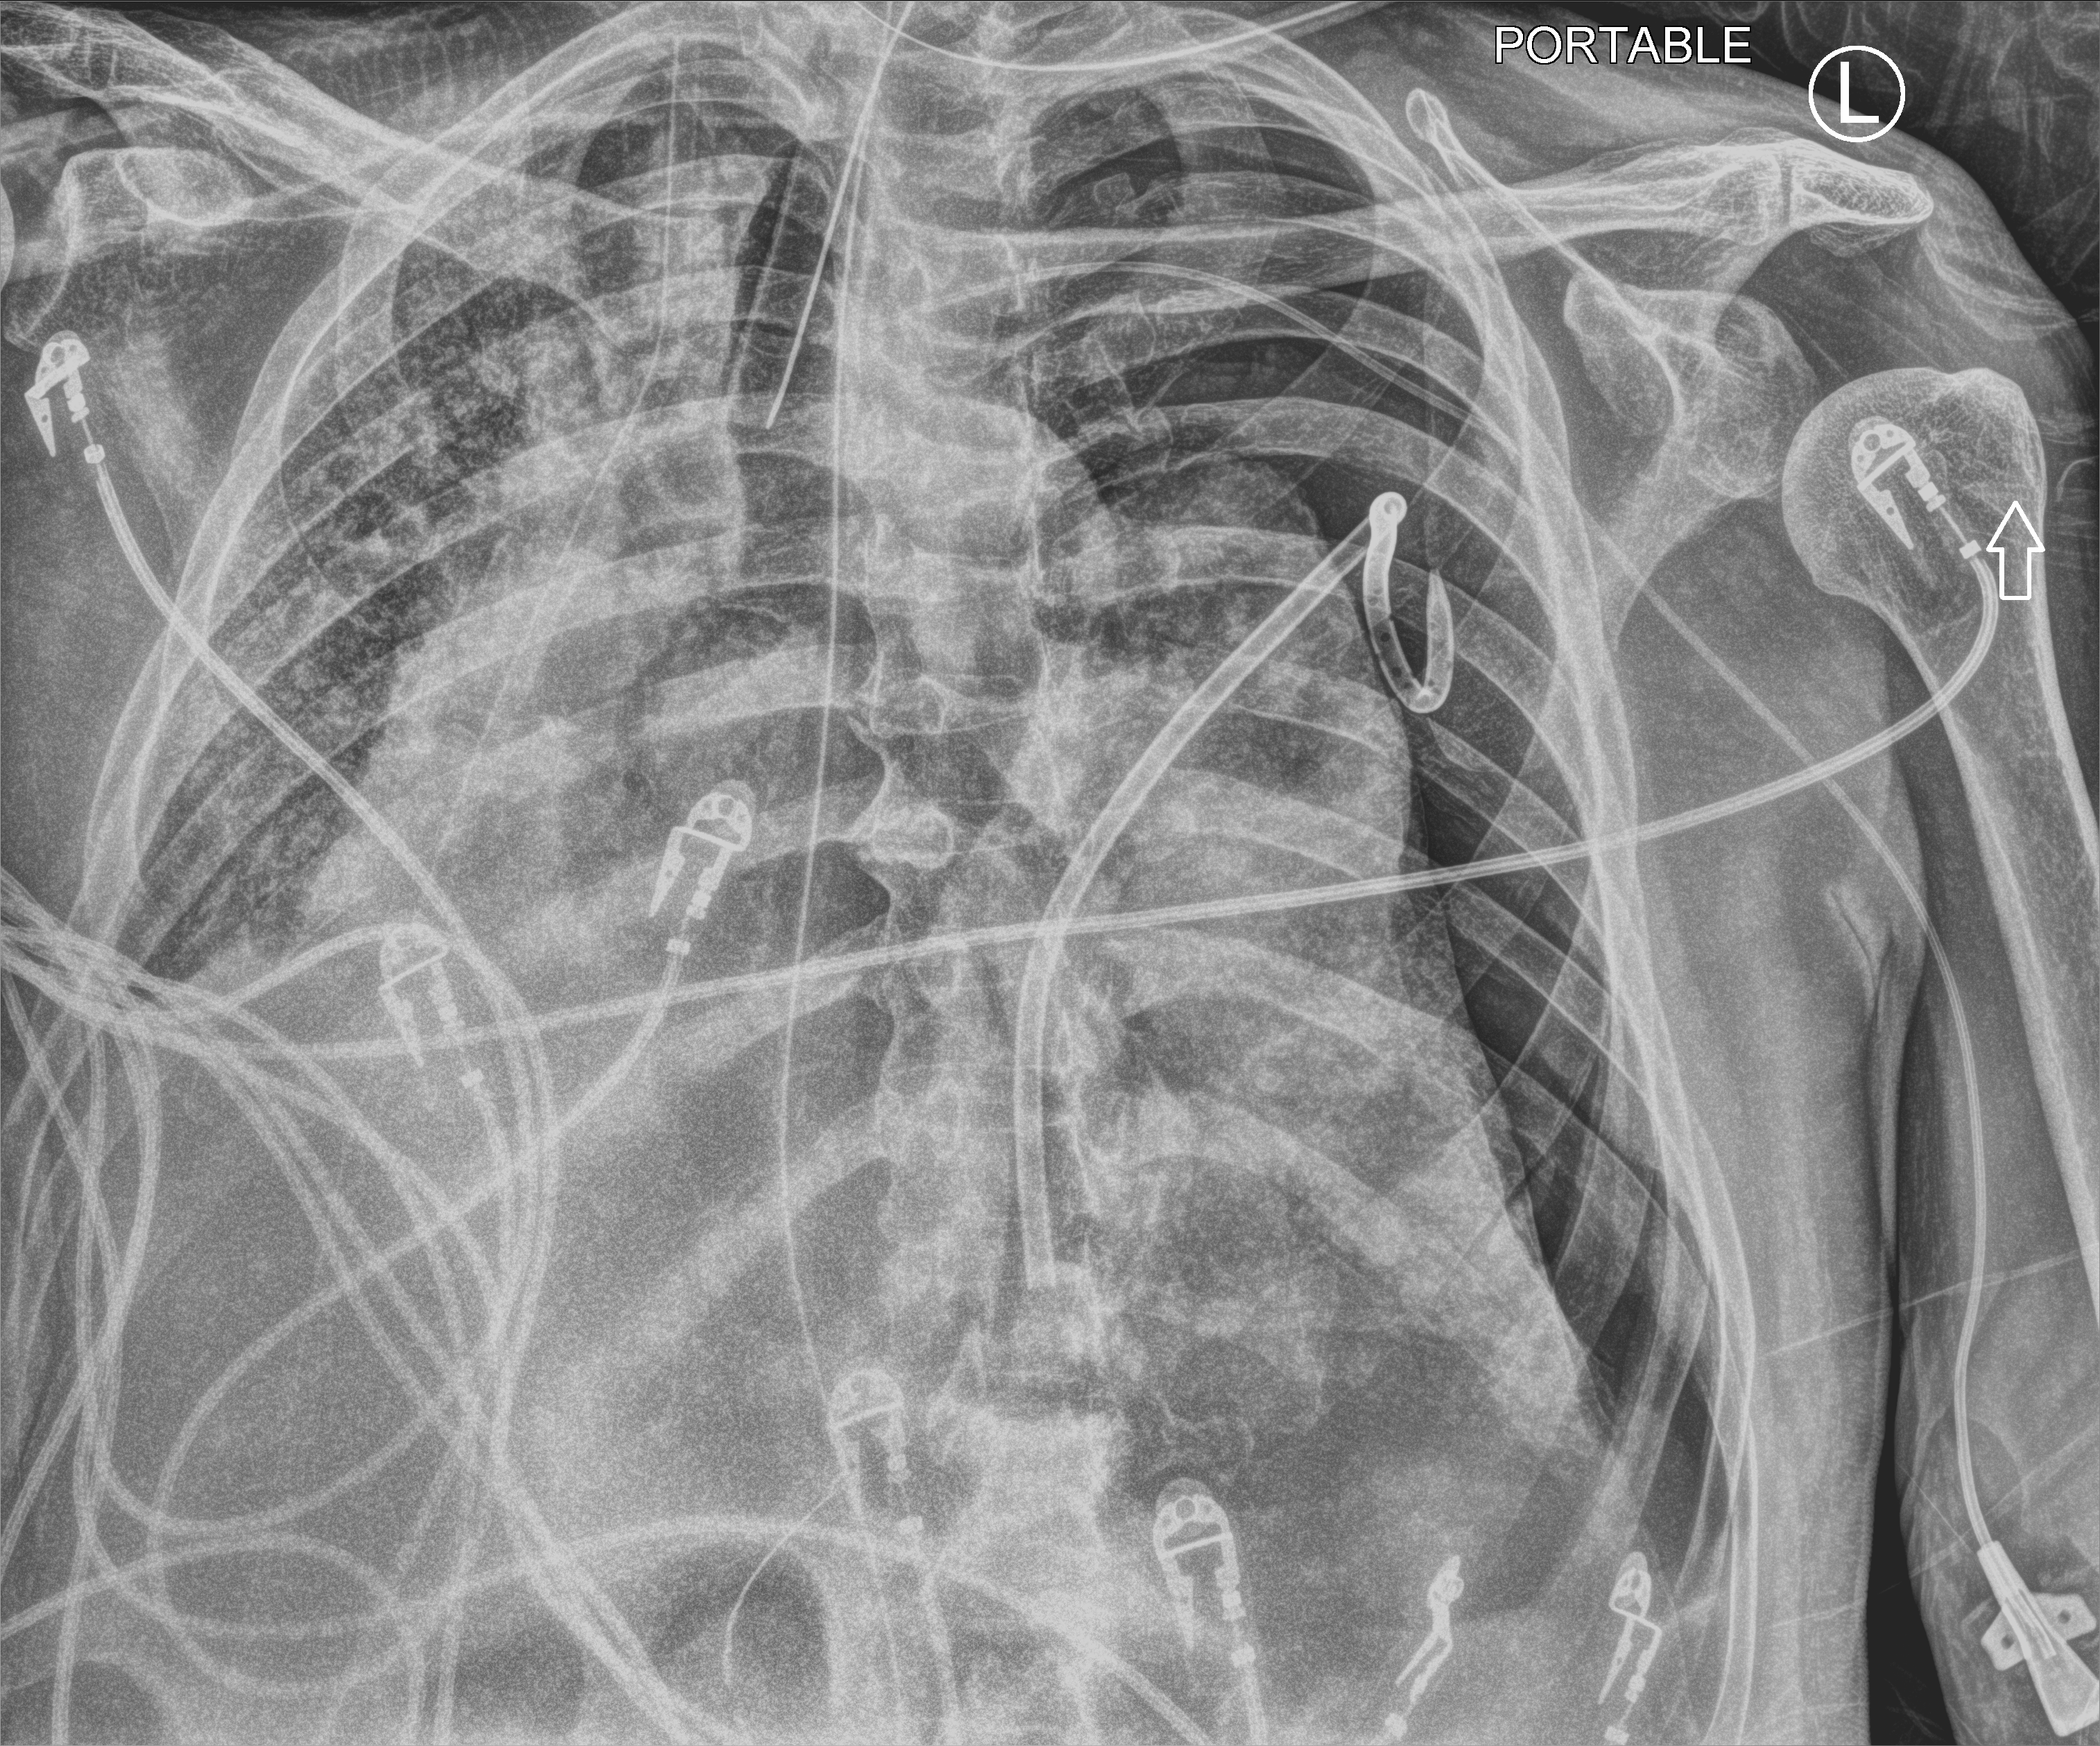
Bedside chest radiograph (computed radiography); anteroposterior (AP) projection. Patient hospitalised with COVID-19; male, aged 60–74 years.
Admission-level facts for this patient (not findings on this image; timing relative to this image not recorded):
- admitted to intensive care during this hospital stay: yes